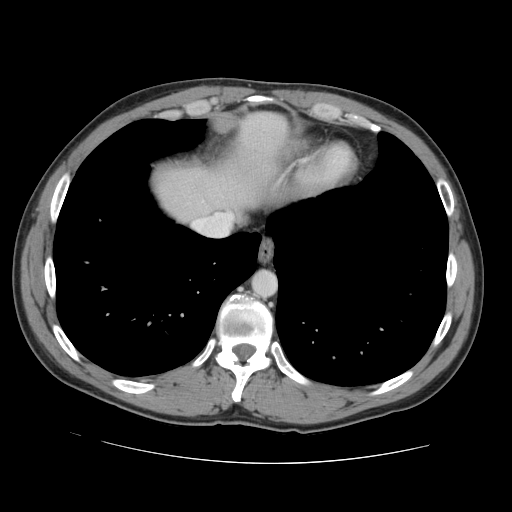
Contrast-enhanced abdominal CT, one axial slice. Slice 128 of 131 in the series (ordered by position). 120 kVp. Intravenous contrast given. Soft-tissue window (W 400 / L 40 HU). 2.5 mm slice thickness. 512 × 512 image matrix. Male patient, age 40 years. Case-level facts recorded for this patient, not image findings: diagnosis: colorectal cancer liver metastases, imaged before liver resection; multiple liver metastases: yes; largest metastasis: 2.9 cm.
Annotated regions visible in this slice (expert manual segmentation):
- hepatic veins: box from (x=193, y=213) to (x=233, y=236) px
- liver: (x=155, y=115)–(x=287, y=220)
- planned liver remnant (the part of the liver to remain after resection): (x=155, y=115)–(x=288, y=218)